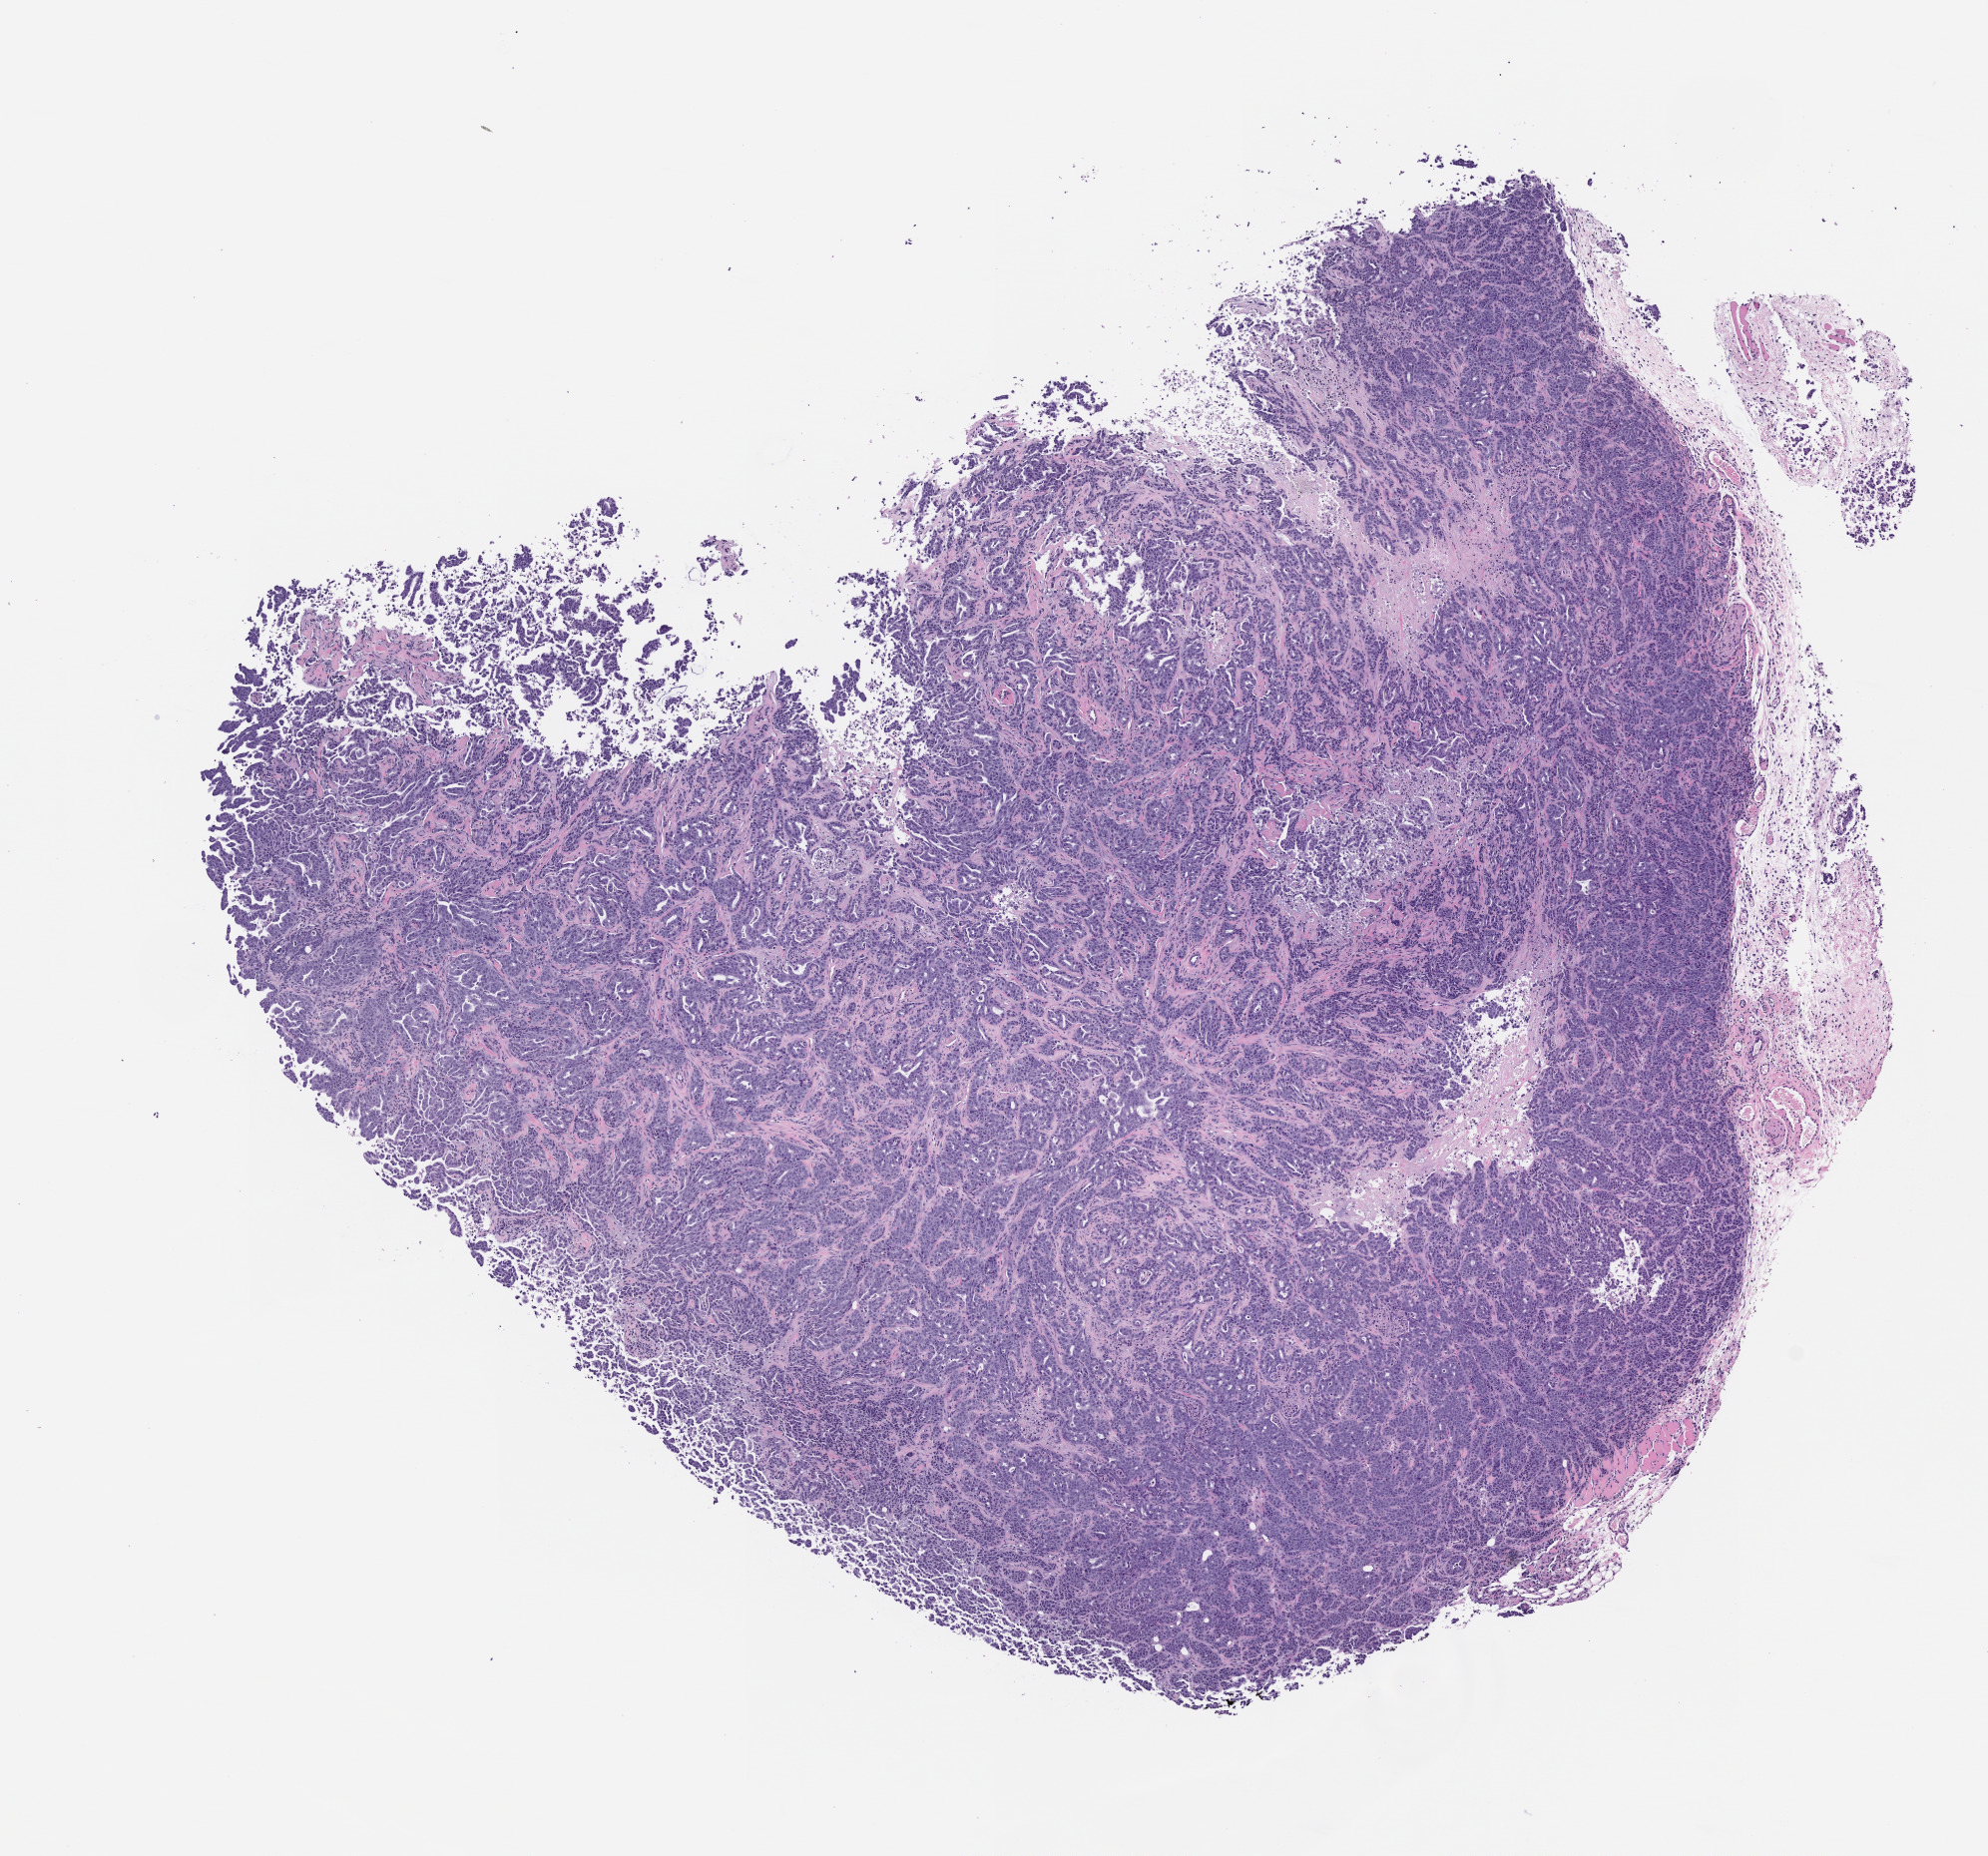
Whole-slide image, hematoxylin and eosin (H&E): patient-derived xenograft (human tumor grown in a mouse), shown as a low-resolution overview of the whole scanned area (about 8.0 x 7.5 mm); formalin-fixed, paraffin-embedded (FFPE) tissue; tumor site category: lung.
- originating patient diagnosis: Lung Adenocarcinoma